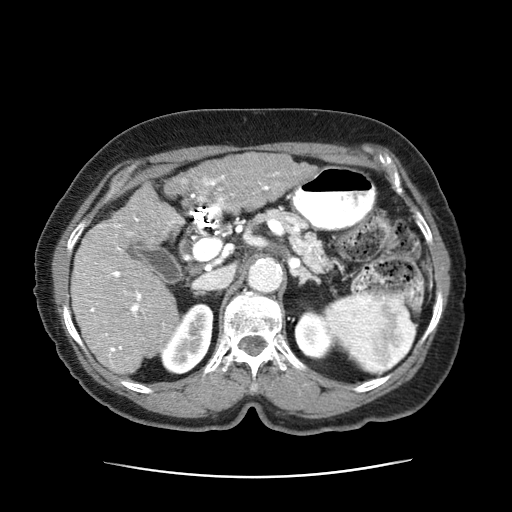
Contrast-enhanced abdominal CT (liver protocol), one axial slice. Position 29 of 63 along the scan axis. Reconstruction kernel STANDARD. 120 kVp. Intravenous contrast given. Soft-tissue window (W 400 / L 40 HU). 2.5 mm slice thickness. 512 × 512 image matrix, field of view 360 × 360 mm. Female patient, age 79 years. Case-level facts recorded for this patient, not image findings: diagnosis: hepatocellular carcinoma (patient treated with transarterial chemoembolisation; whether this scan precedes or follows treatment is not stated here); TNM stage (as recorded): Stage-II; Child-Pugh class: B; tumour nodularity: multinodular; tumour size: 5 cm.
Outlined on this slice (semi-automatically segmented with operator editing):
- abdominal aorta: bounding box [x1, y1, x2, y2] px = [248, 256, 281, 293]
- liver parenchyma outside the tumour (the mass and vessels are separate outlines, so this box may not span the whole liver): [71, 182, 186, 379]
- mass: [160, 152, 318, 209]
- liver vessels: [83, 175, 225, 358]